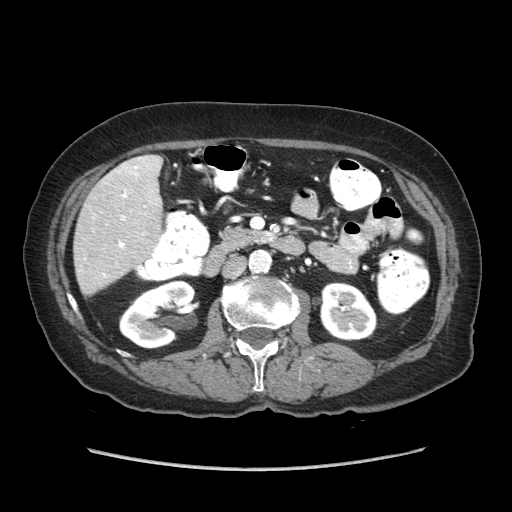
Contrast-enhanced abdominal CT (liver protocol), one axial slice; position 22 of 89 along the scan axis; soft-tissue window (W 400 / L 40 HU); 2.5 mm slice thickness; 512 × 512 image matrix, field of view 360 × 360 mm. From the clinical record (not read from this slice): diagnosis: hepatocellular carcinoma (patient treated with transarterial chemoembolisation; whether this scan precedes or follows treatment is not stated here); TNM stage (as recorded): Stage-IIIA; Child-Pugh class: A; tumour nodularity: multinodular.
Annotated regions visible in this slice (semi-automatically segmented with operator editing):
- liver parenchyma outside the tumour (the mass and vessels are separate outlines, so this box may not span the whole liver): bounding box (x1, y1, x2, y2) in pixels: (74, 154, 162, 294)
- liver vessels: (104, 158, 141, 277)